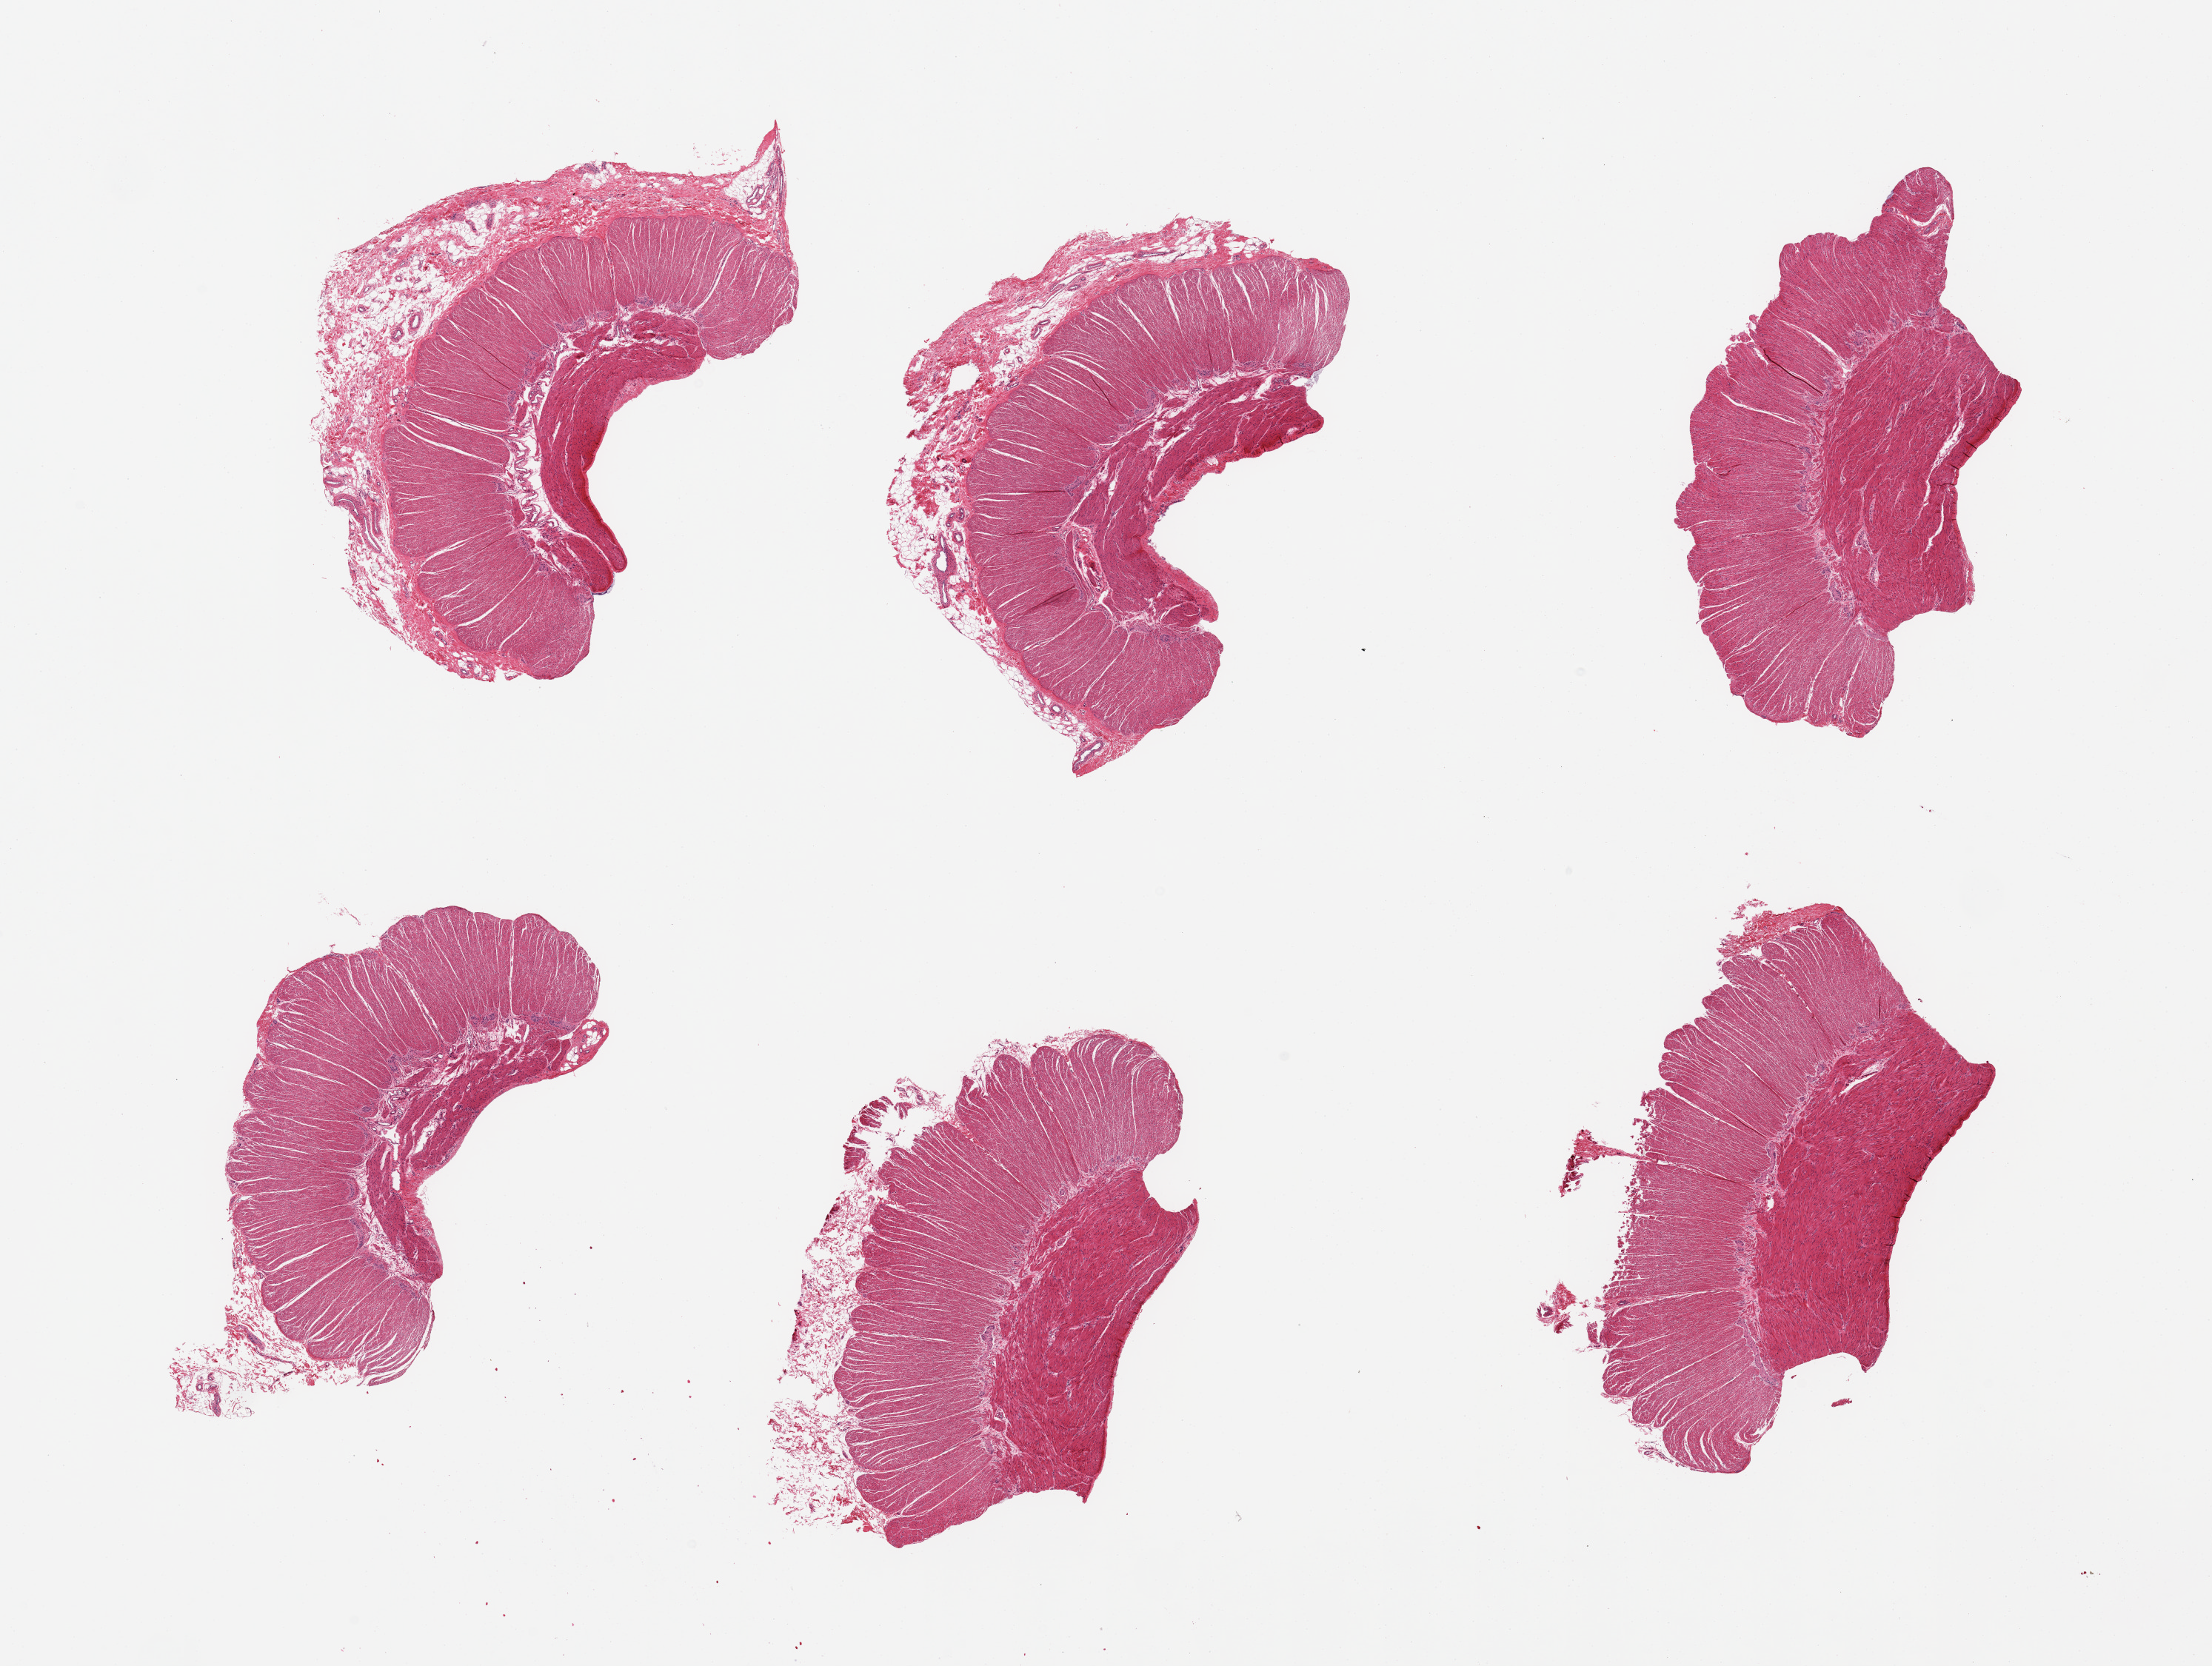
Whole-slide image, hematoxylin and eosin (H&E) stain, low-resolution overview of the scanned area, about 23.6 x 17.8 mm (from a 20x scan); PAXgene-fixed, paraffin-embedded tissue; sampled site (target tissue): sigmoid colon; tissue donor sample.
Pathologist's review note for this sample: 6 pieces, all target muscularis.